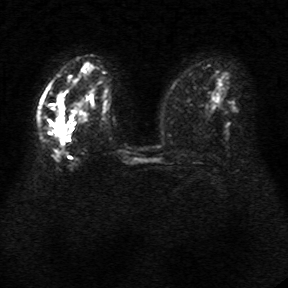
Breast MRI, one axial slice; diffusion-weighted series; image 2 of 4 stored at this slice position (different b-values; order by instance number); 1.5 T; 5 mm slice thickness; 288 × 288 image matrix, field of view 340 × 340 mm. Female patient.
Outlined on this slice (expert manual segmentation):
- tumour on diffusion-weighted imaging: bounding box <47,95,67,138> (left, top, right, bottom; pixels)